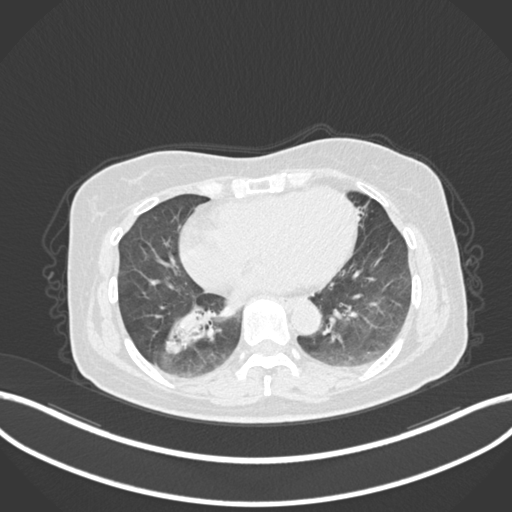
Chest CT, one axial slice. Slice 52 of 222 in the series (ordered by position). Reconstruction kernel B30f. 120 kVp. Lung window (W 1500 / L -600 HU). 512 × 512 image matrix. Patient: female, 67 years. Case-level facts recorded for this patient, not image findings: clinical TNM (as recorded): T1c N1 M0.
Structures marked on this image (rectangle marked by the reading radiologist):
- lung tumour (recorded histology: adenocarcinoma): box from (x=159, y=300) to (x=219, y=361) px